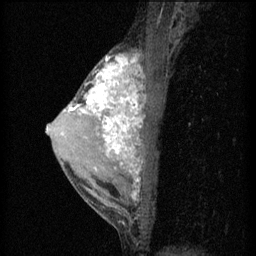
Breast MRI (dynamic contrast-enhanced), one sagittal slice. Slice 35 of 60 in the series (ordered by position). 3 images stored at this slice position (order not interpretable as contrast timing). 1.5 T. TE 4.2 ms, TR 11 ms. 2 mm slice thickness. 256 × 256 image matrix, field of view 180 × 180 mm. Patient: female, 40 years.
Outlined on this slice (semi-automatic segmentation, software-assisted and operator-edited):
- analysis volume of interest (the breast-tissue region the enhancement analysis was run in; not a lesion): bounding box (x1, y1, x2, y2) in pixels: (55, 50, 153, 203)
- tumour enhancement mask (voxels above the 70 % enhancement threshold inside the analysis volume of interest): (64, 56, 145, 201)